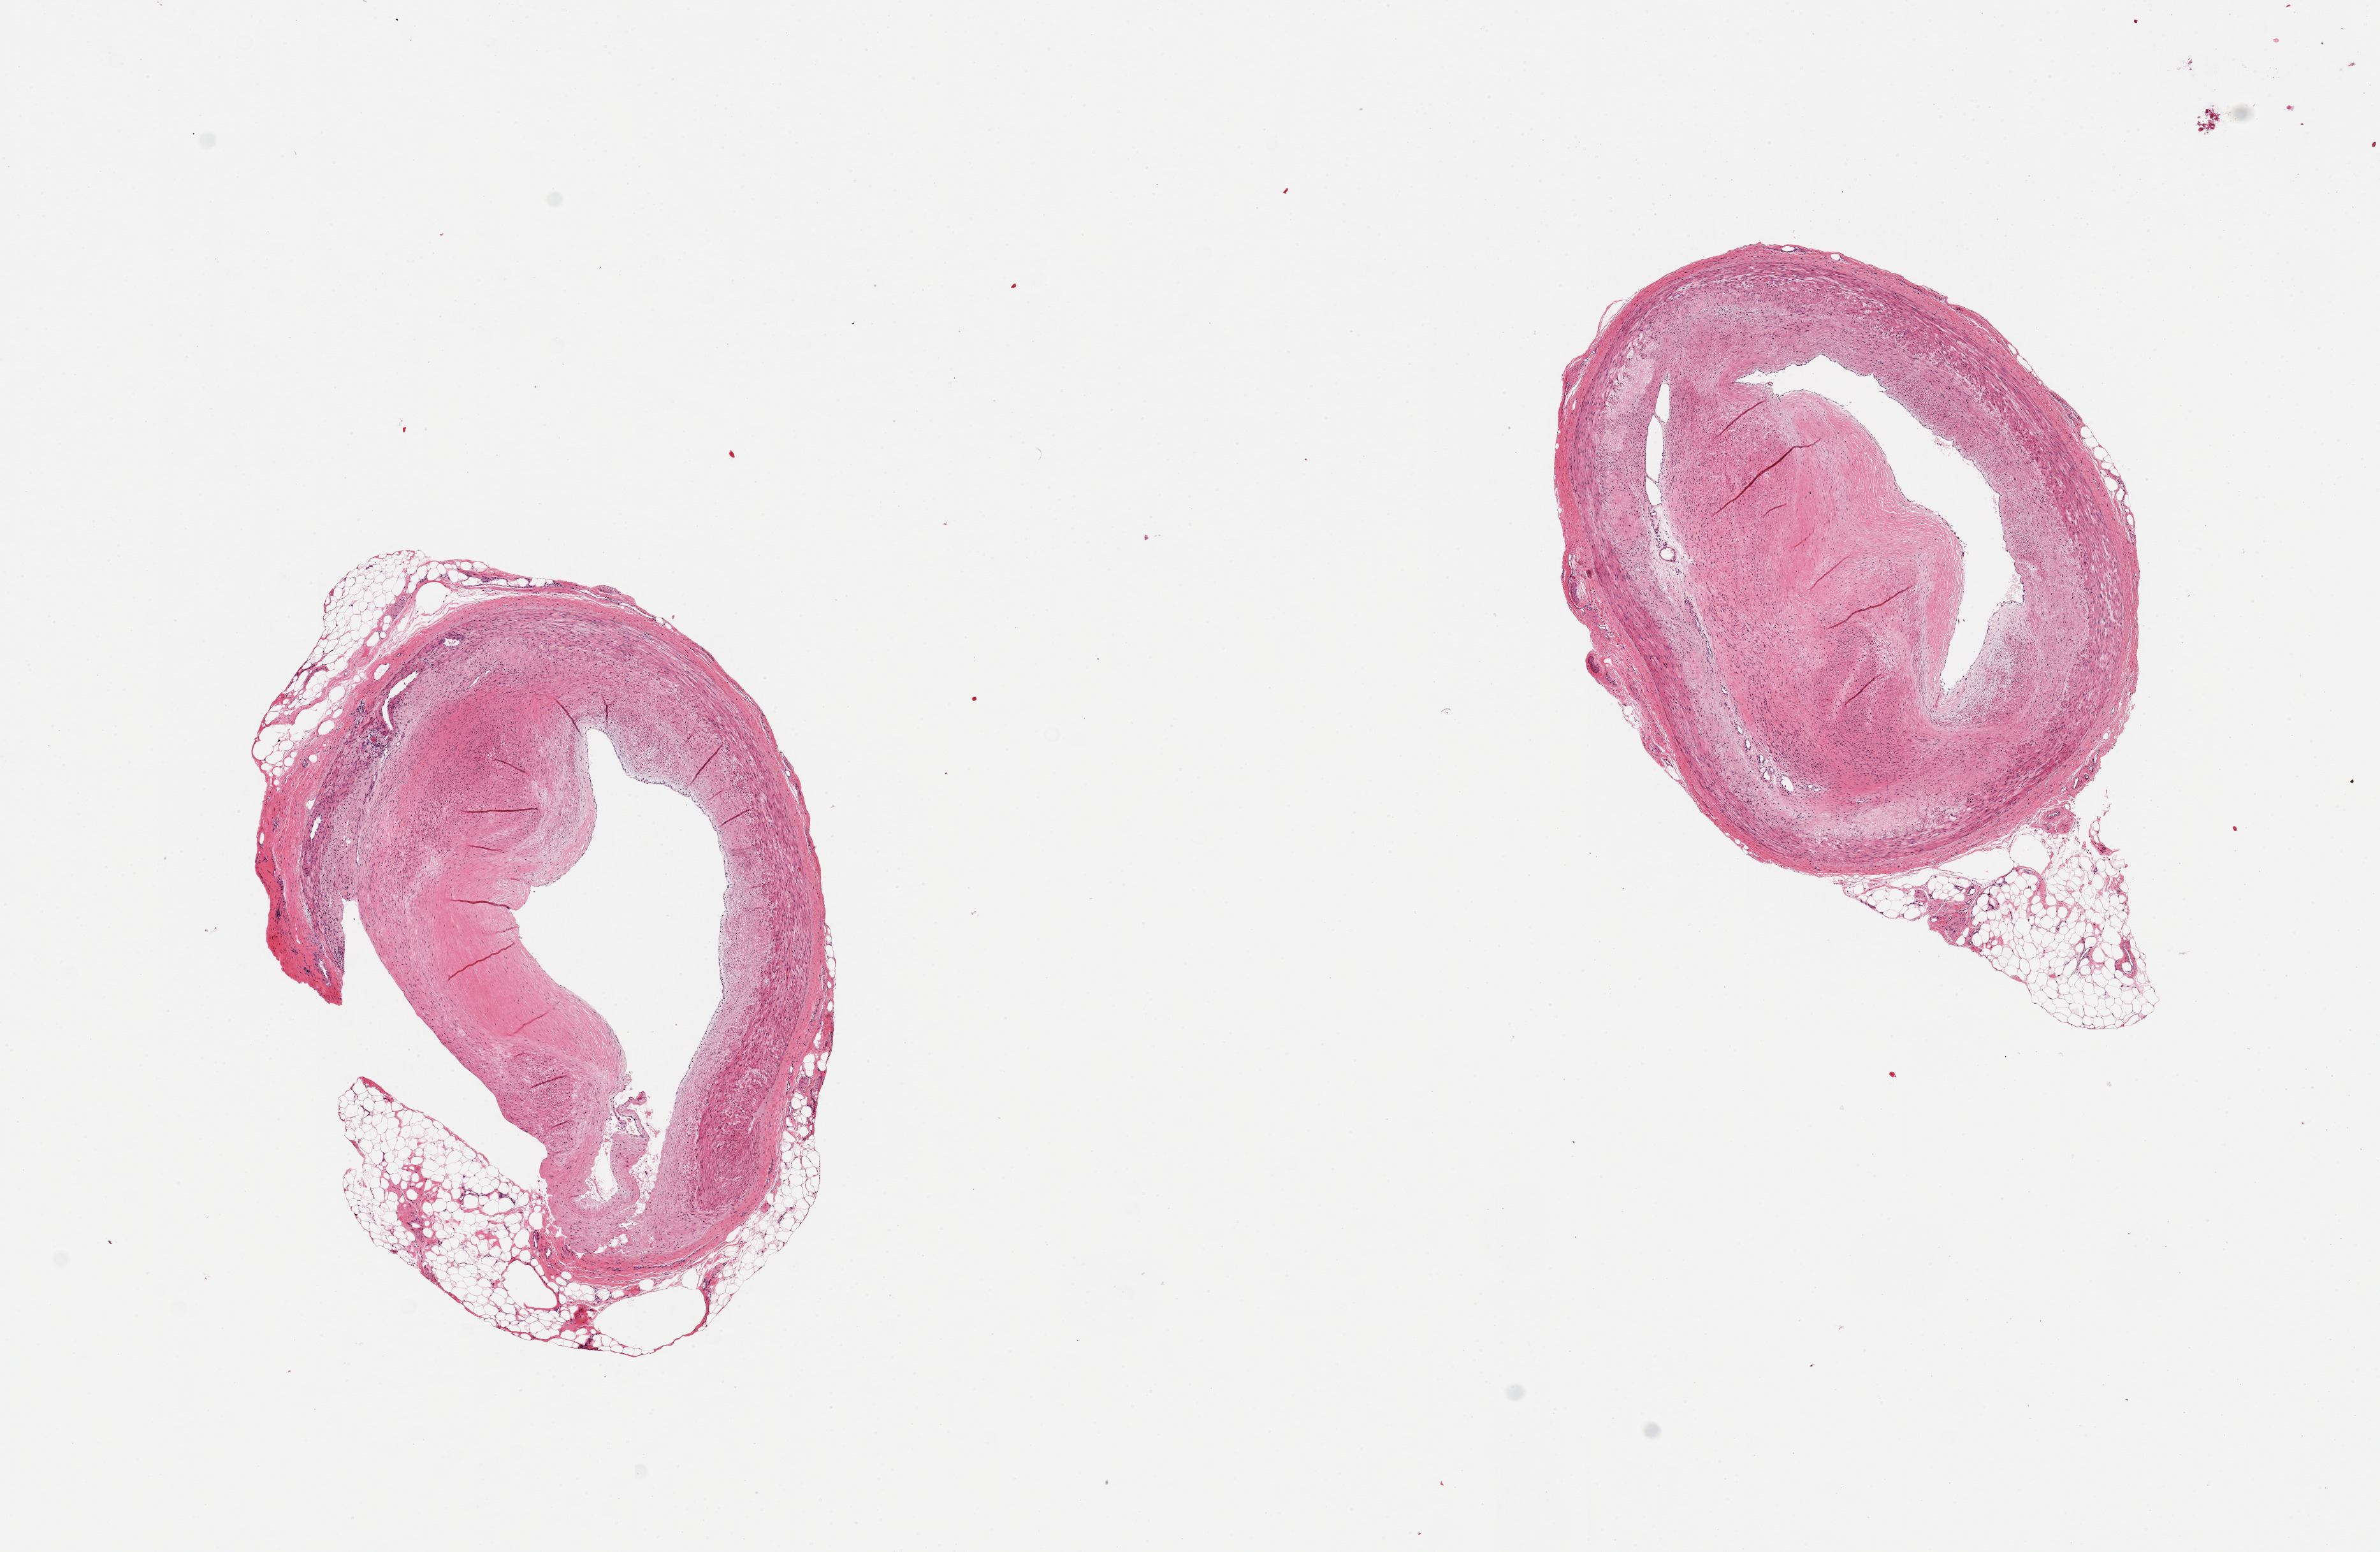
Whole-slide image, H&E stain, brightfield — low-resolution overview of the scanned area, about 14.8 x 9.6 mm (from a 20x scan), PAXgene-fixed, paraffin-embedded tissue, sampled site (target tissue): coronary artery, tissue donor sample. Donor sex: male.
Review note (as recorded): 2 pieces; large eccentric plaque narrows lumen by 80%. 1 mm extraneous fat nodule on vessel's outer edge.